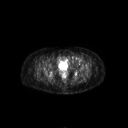
FDG PET of an extremity soft-tissue mass (from a PET/CT study), one axial slice; slice 55 of 267 in the series (ordered by position); 3.27 mm slice thickness; 128 × 128 image matrix. Patient: female, 47 years. From the clinical record (not read from this slice): histological type: myxofibrosarcoma; grade: intermediate; site of the primary tumour: left thigh.
Outlined on this slice (expert contour drawn on MRI and transferred to this co-registered scan by the dataset authors):
- gross tumour volume including surrounding oedema: bounding box <67,58,82,63> (left, top, right, bottom; pixels)